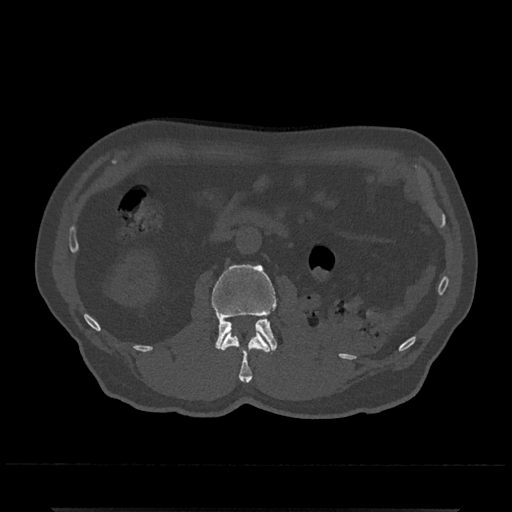
CT including the spine, one axial slice. Position 317 of 797 along the scan axis. 120 kVp. Bone window (W 1800 / L 400 HU). 0.5 mm slice thickness. 512 × 512 image matrix, field of view 393 × 393 mm. Patient: male, 67 years. From the clinical record (not read from this slice): primary cancer: prostate.
Annotated regions visible in this slice (semi-automatically segmented with operator editing):
- L1 vertebra: bounding box [x1, y1, x2, y2] px = [221, 330, 270, 383]
- L2 vertebra: [211, 264, 278, 354]